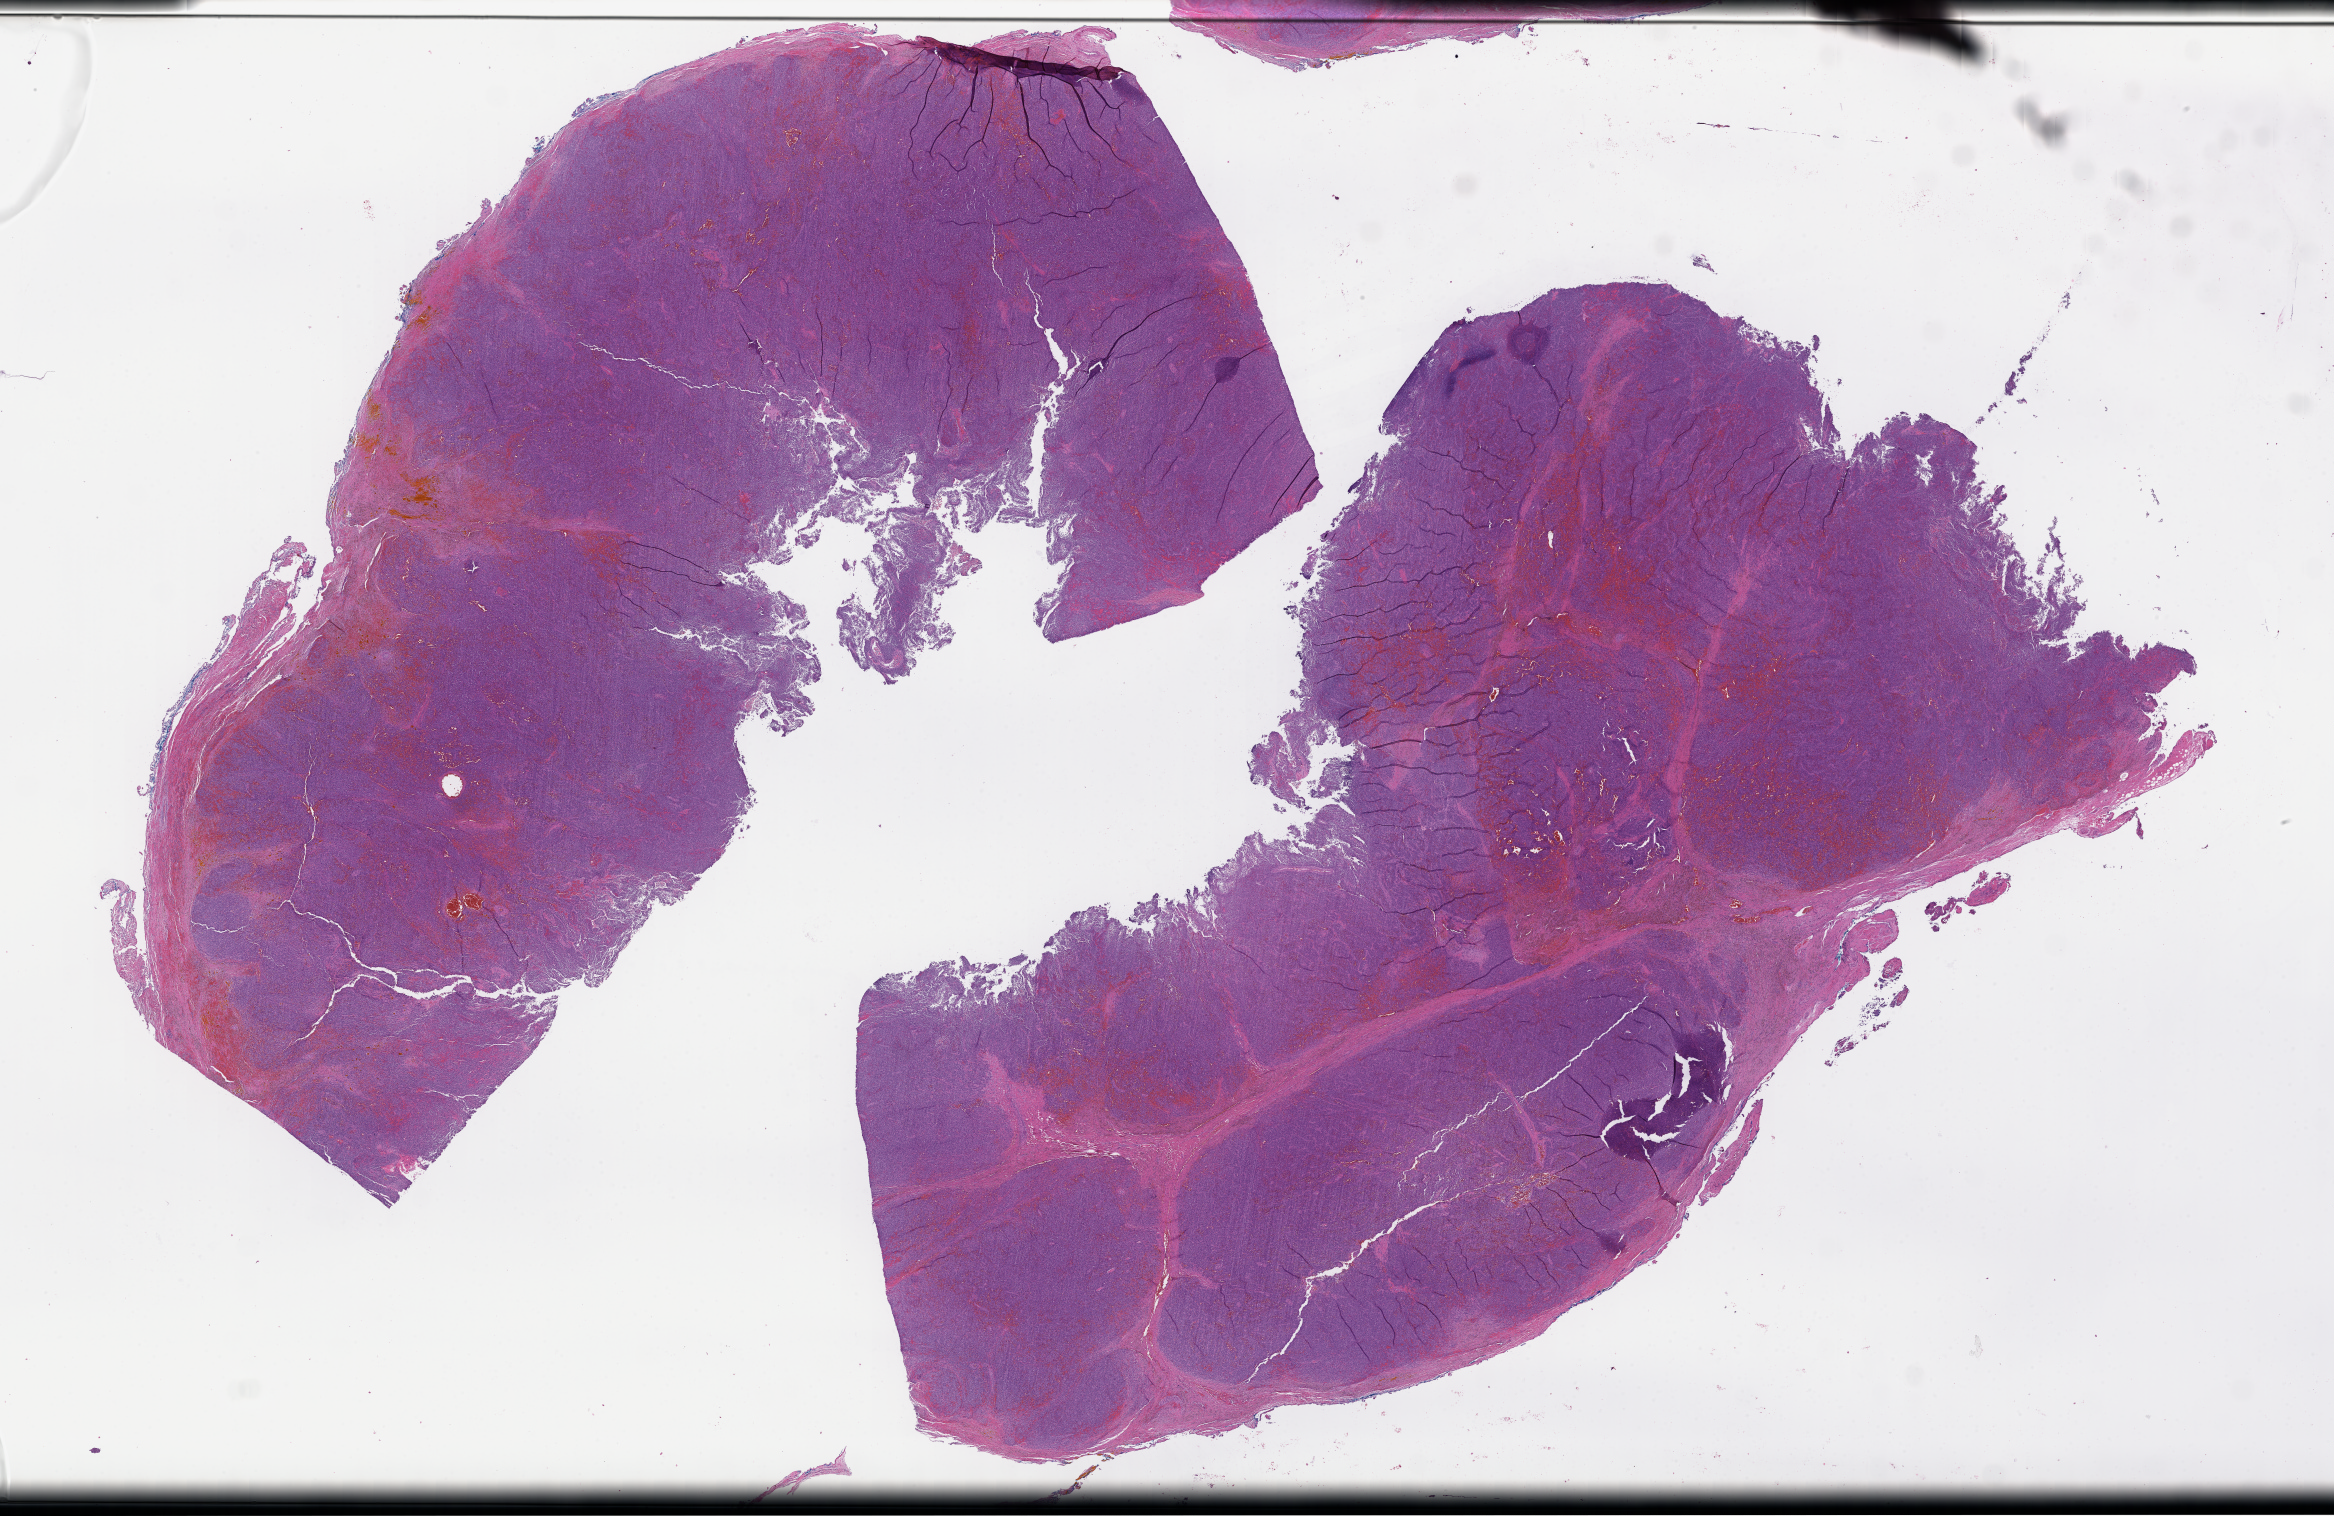
Digitized haematoxylin and eosin-stained section — shown as a low-resolution overview of the whole scanned area (about 37.7 x 24.5 mm). FFPE section. Patient sex: male.
This section: metastasis (sampled organ not recorded). Primary diagnosis of the patient: Plasma Cell Myeloma.